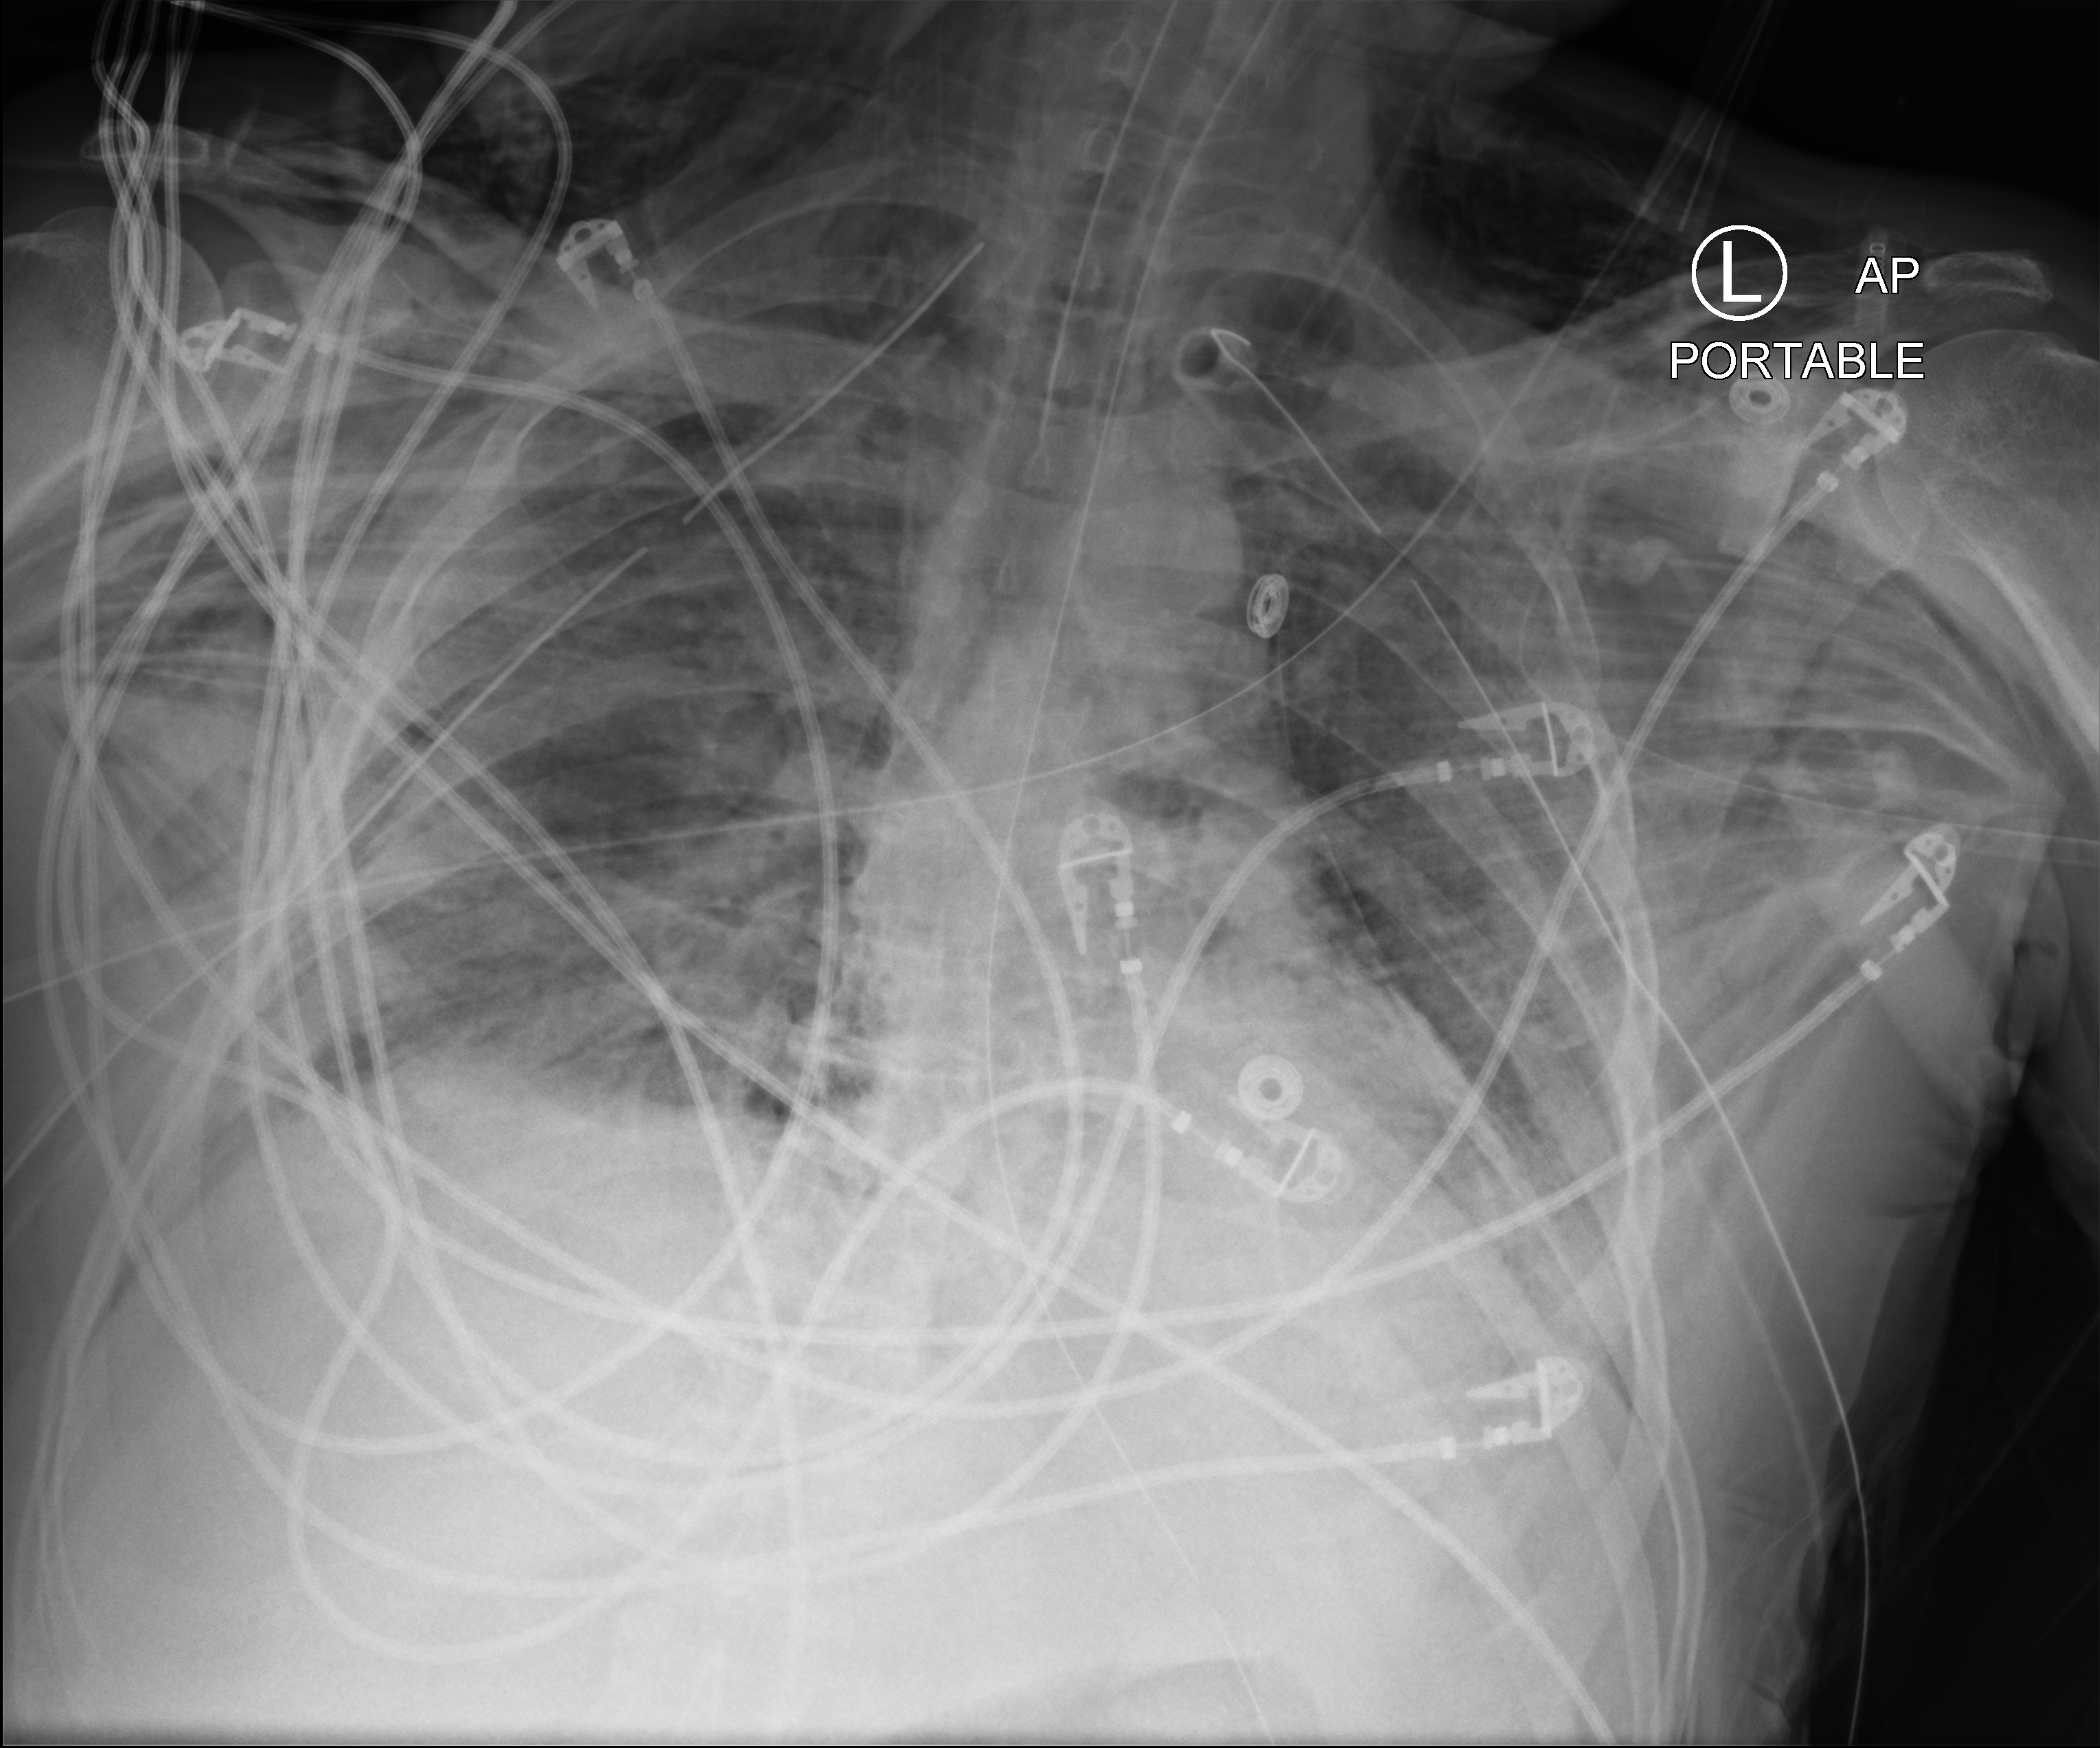
Chest X-ray (portable); anteroposterior (AP) projection. Patient hospitalised with COVID-19; male, aged 18–59 years.
From the hospital-stay record, not from the radiograph (when in the stay this image was taken is not recorded): length of hospital stay: 83 days; mechanically ventilated during this hospital stay: yes; COPD (admission record): no.